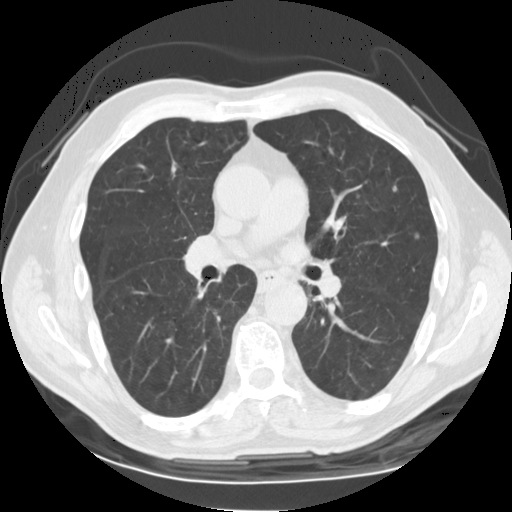
Chest CT (low-dose screening protocol), one axial image; baseline annual screen; lung window (W 1500 / L -600 HU); 2.5 mm slice thickness; standard (soft-tissue) reconstruction kernel (STANDARD); slice 68 of 141 in the series. Male participant, aged 71 years at enrolment. Current smoker at enrolment.
Expert-annotated lung lesion, bounding box <400,223,429,254> (left, top, right, bottom; pixels). Screening reader's record for this exam: no non-calcified nodule ≥4 mm recorded. Official screen result: negative screen, minor abnormalities not suspicious for lung cancer. Participant outcome: lung cancer diagnosed 802 days after this screen (after the third annual screen) — adenocarcinoma, NOS, left upper lobe, moderately differentiated (G2), stage IA (AJCC 6th edition), 10 mm at pathology.